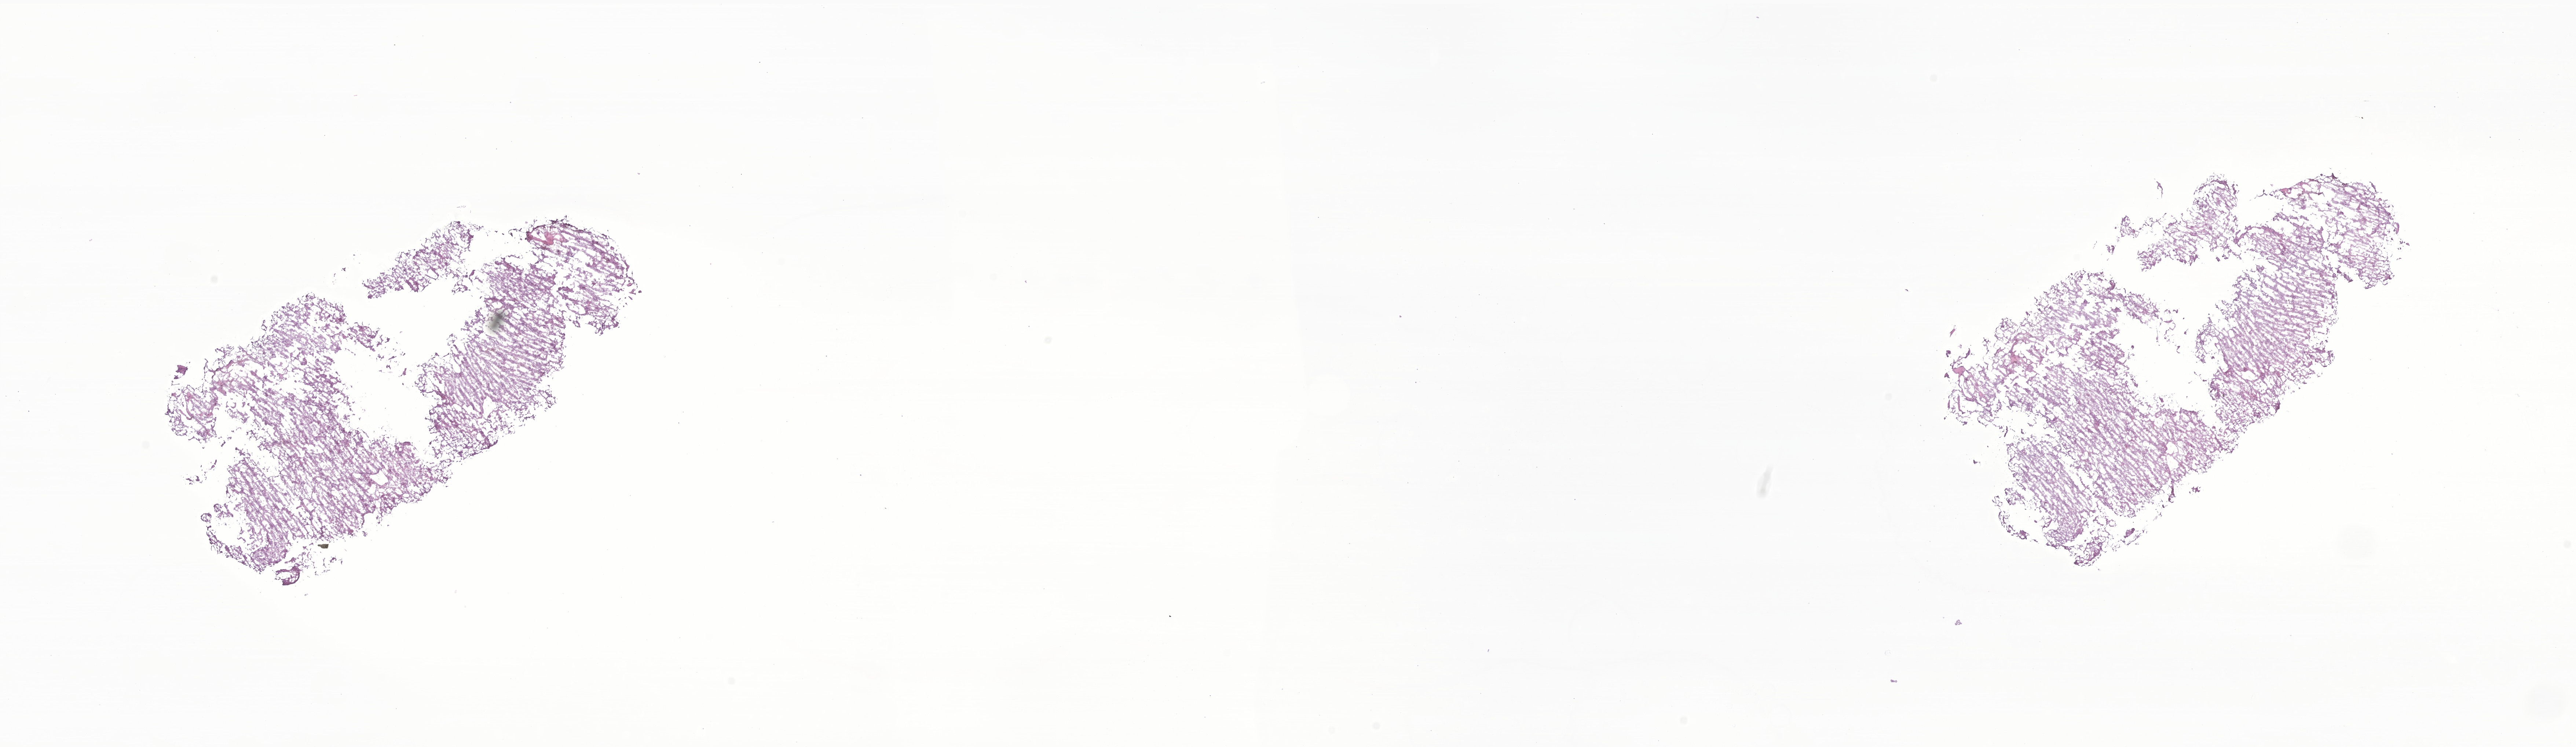
Digitized hematoxylin and eosin (H&E)-stained section of tumor tissue from the vertebral column — low-resolution overview of the scanned area, about 29.6 x 8.6 mm. Cryosection (OCT / tissue freezing medium). Patient male; age 205 months (17 years 1 month).
Diagnosis (ICD-O-3 morphology term): Myxopapillary ependymoma.